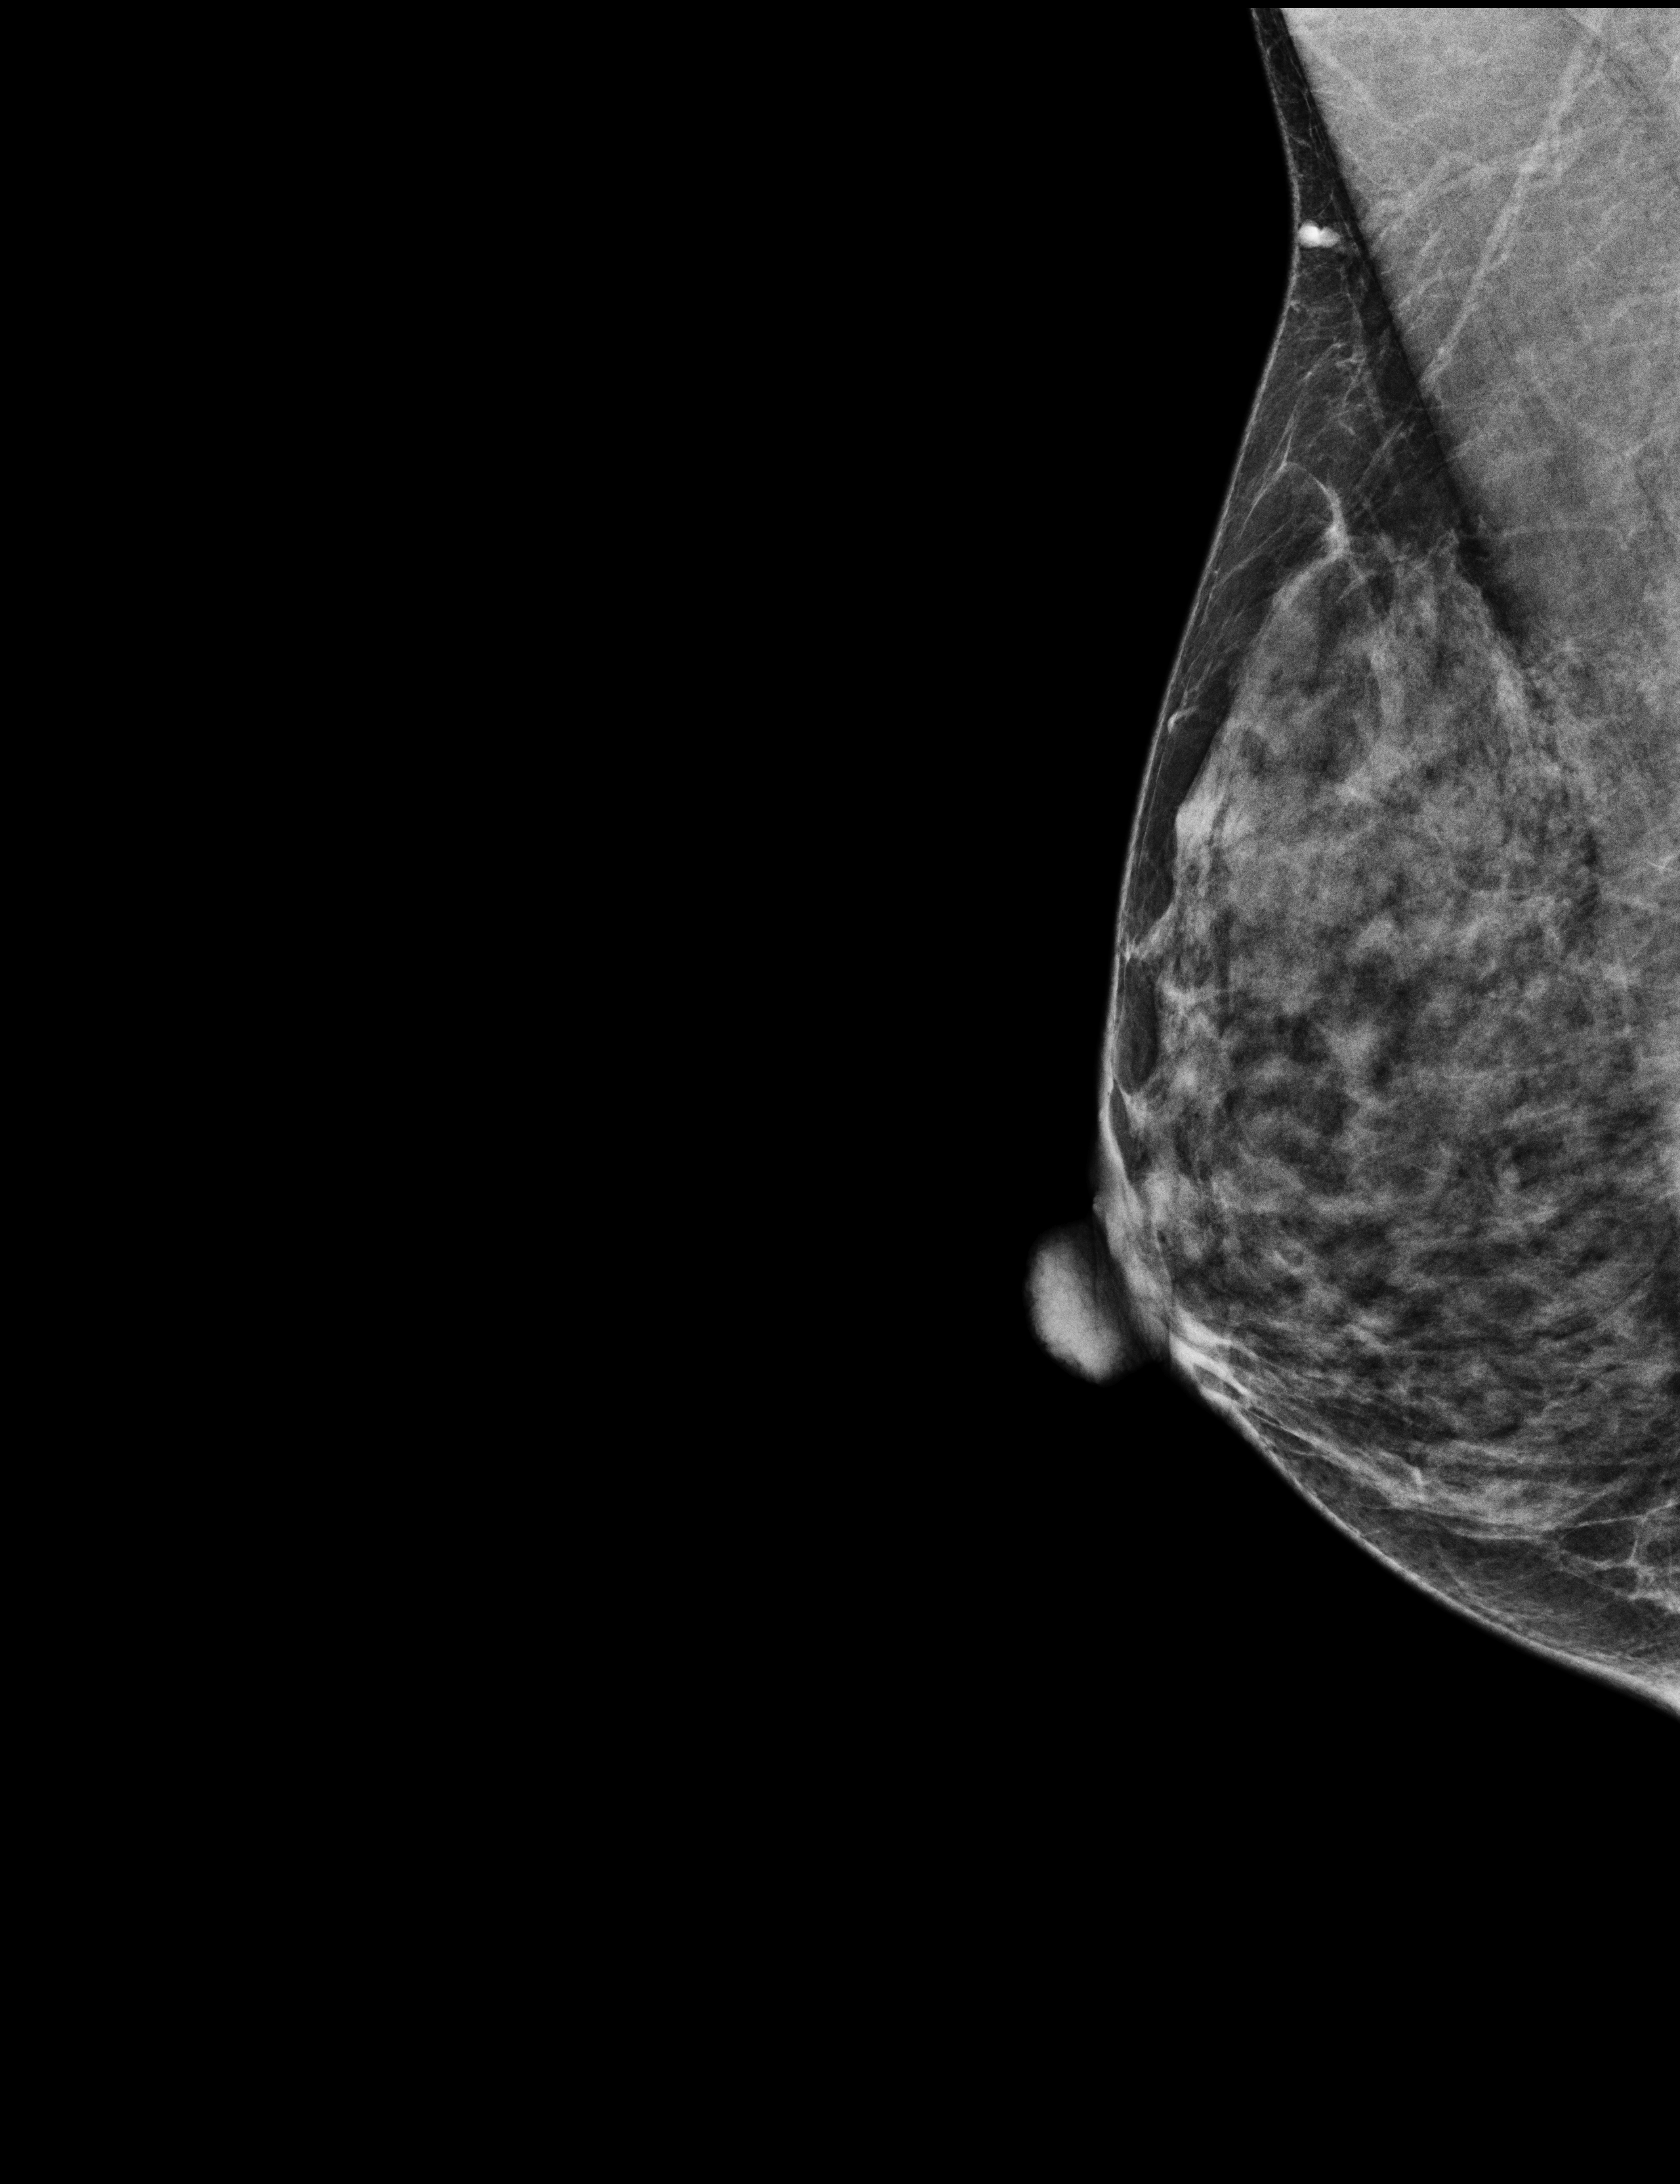
Full-field digital mammogram (FFDM); right breast; mediolateral oblique (MLO) view; annual screening mammography examination; system: Selenia Dimensions. Patient: female, 42 years.
BI-RADS breast density category at the screening exam (both breasts, scale 1–4): 3. Final BI-RADS assessment for this screening round (tomosynthesis exam, both breasts): category 1. Recall: no recall after this screen.